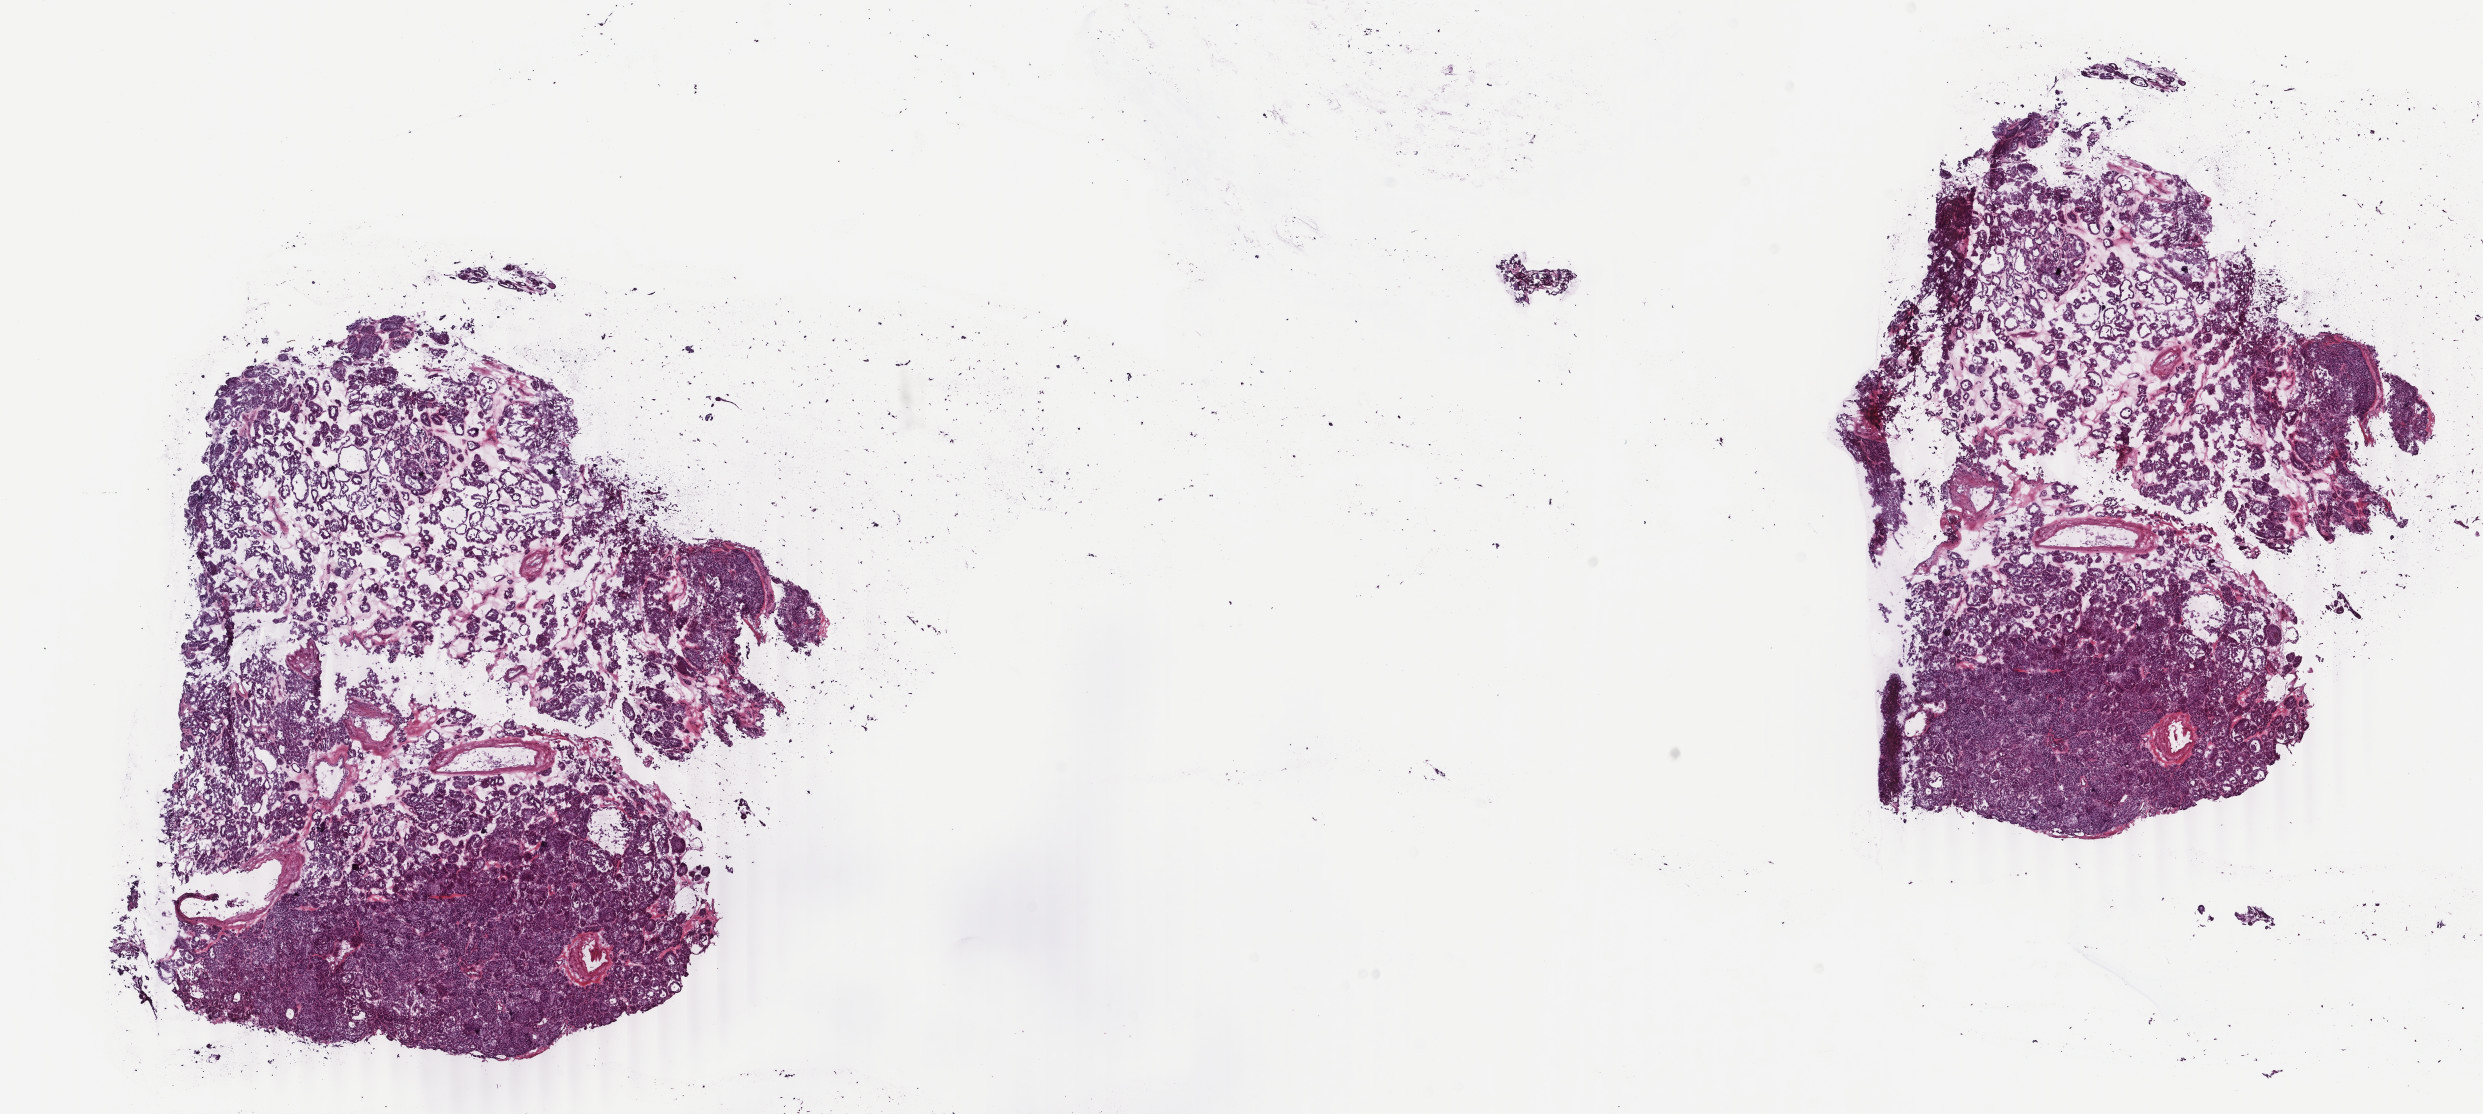
Digitized H&E tissue section (whole slide) — shown as a low-resolution overview of the whole scanned area (about 19.8 x 8.9 mm, slide scanned at 40x); frozen section from the top of the tissue portion; primary tumour sample from the thyroid. Female patient; age at initial diagnosis 68 years. Composition of this section per pathologist review: tumour cells 100%, tumour nuclei 92%, normal cells 0%, stromal cells 0%, necrosis 0%. Inflammatory infiltration, as recorded: lymphocyte infiltration 0%, monocyte infiltration 0%, neutrophil infiltration 0%.
TNM: T1b N0 MX. Lymph nodes positive (case pathology): 0 of 2 examined. AJCC pathologic stage: I. Diagnosis: Papillary carcinoma, follicular variant (thyroid gland).